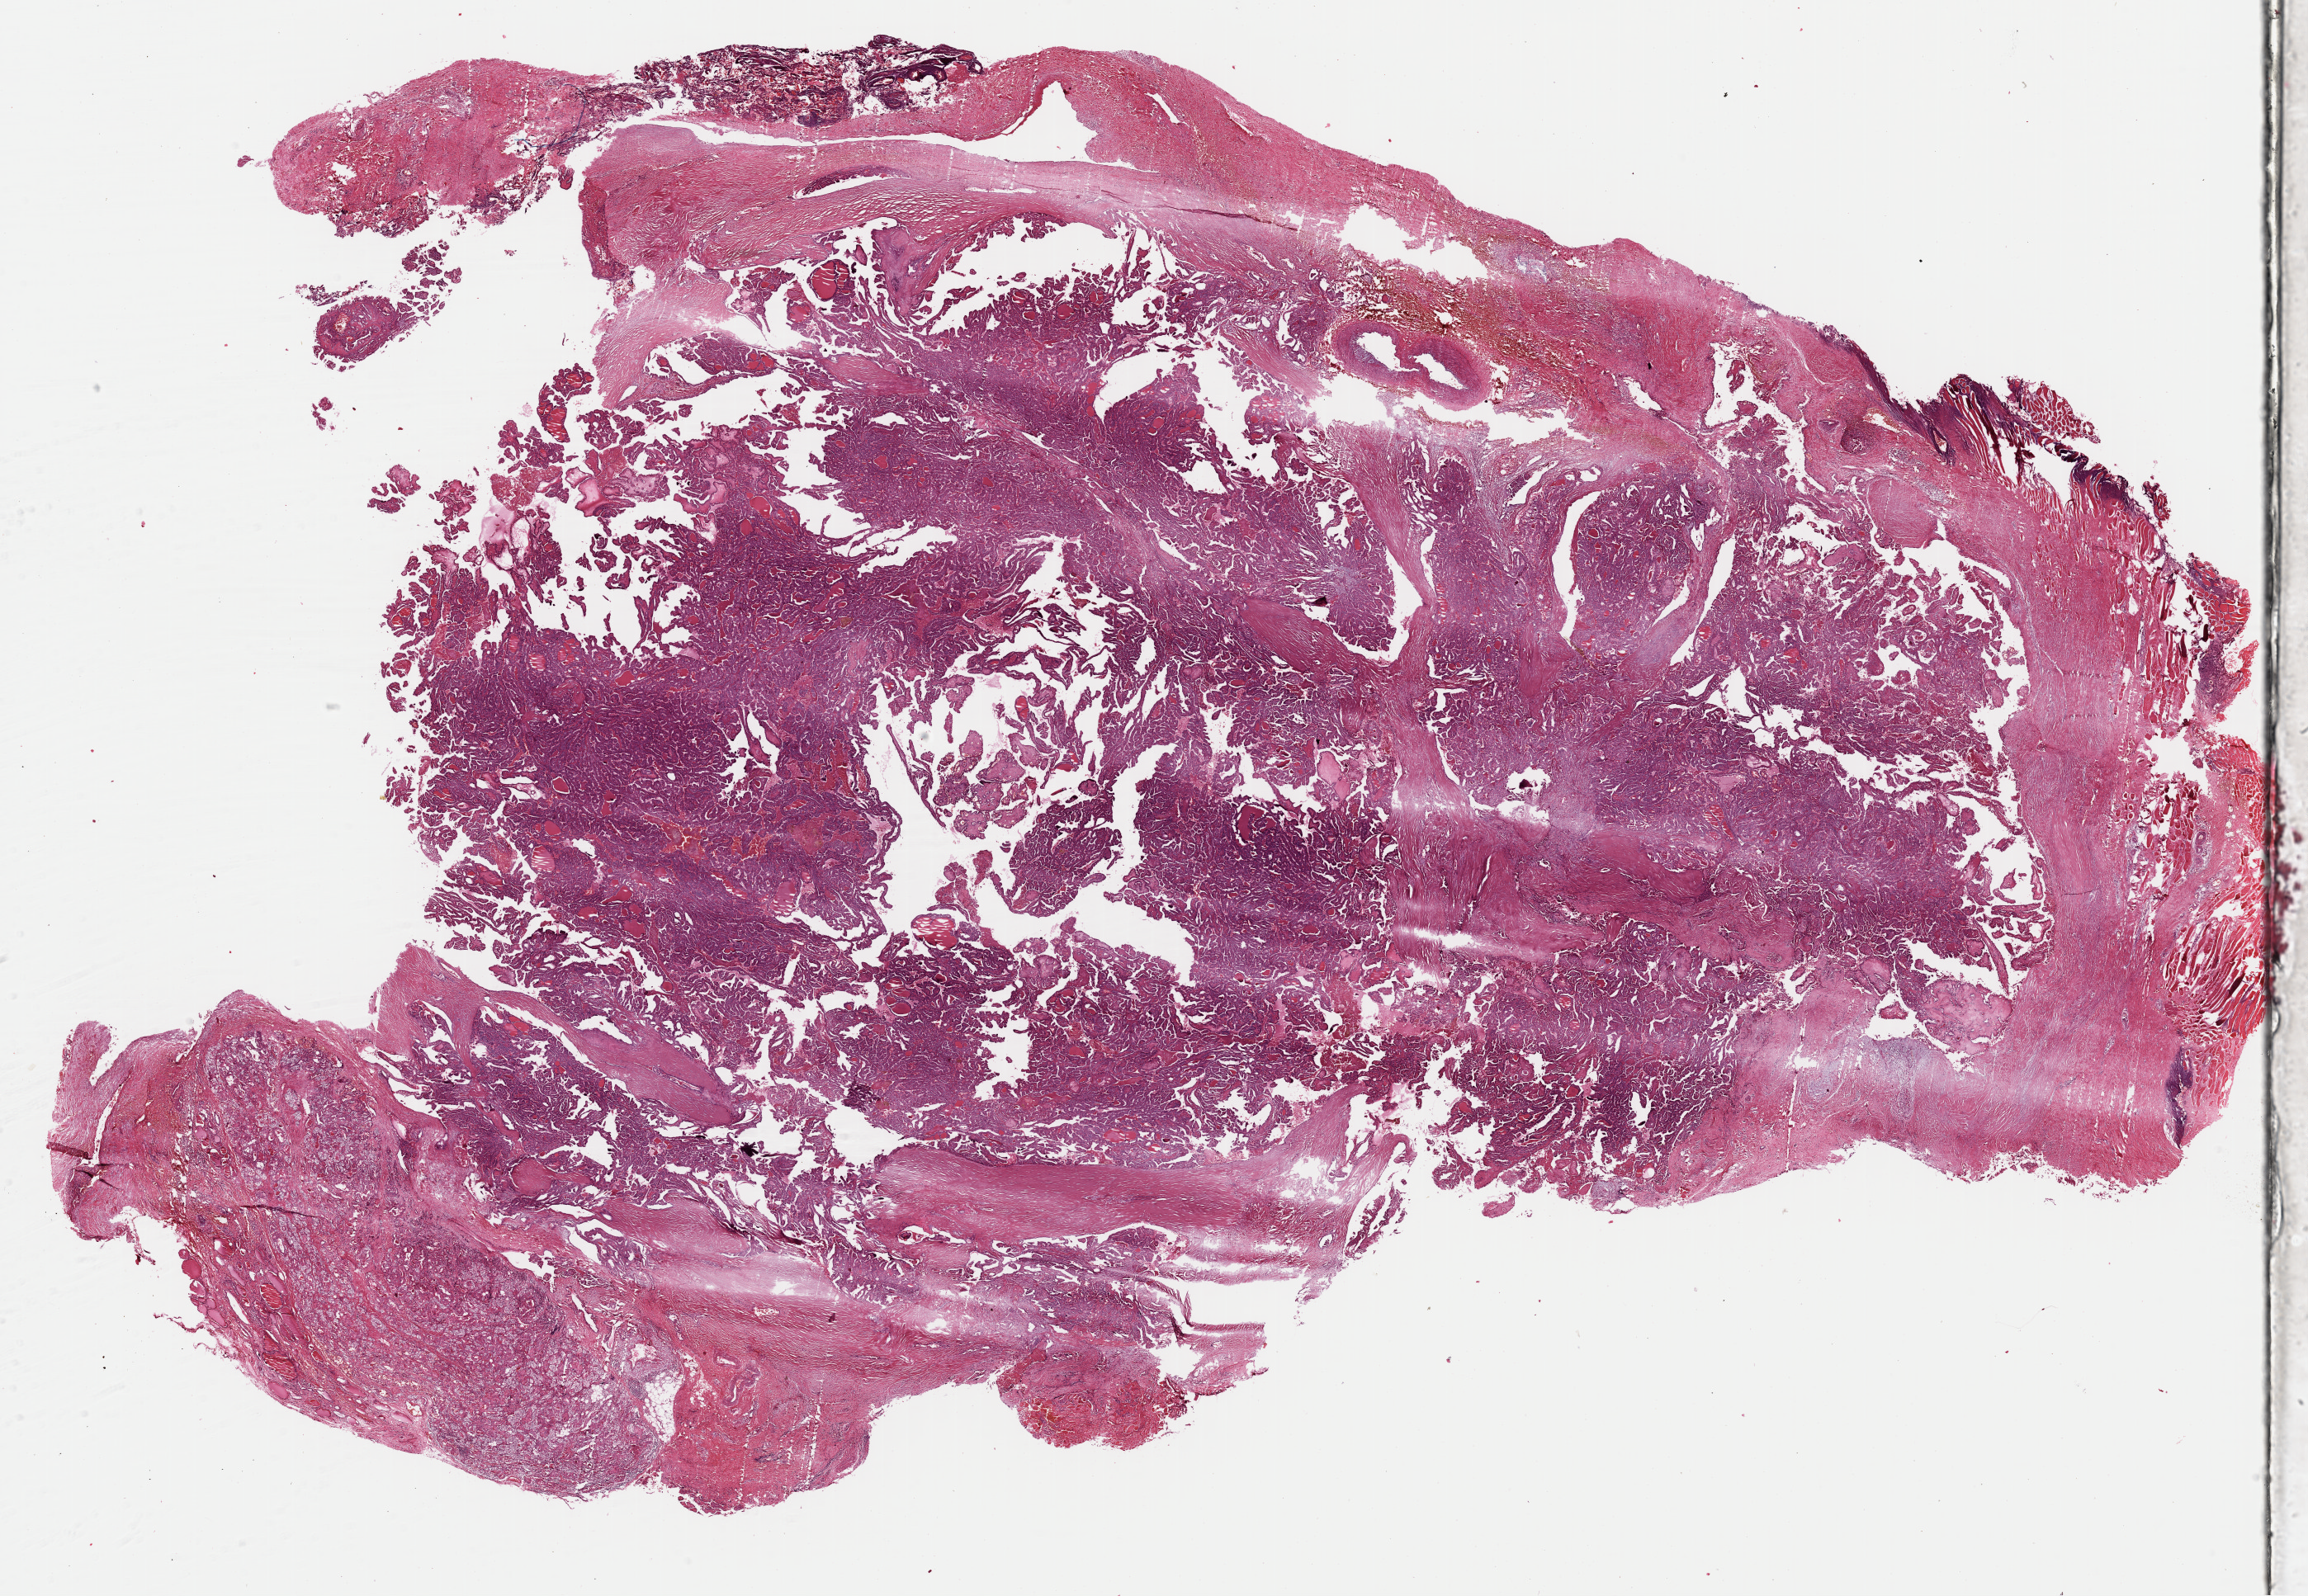
H&E-stained whole-slide image — whole scanned area (about 22.1 x 15.3 mm, acquisition: 40x scan) shown as a low-resolution overview. Formalin-fixed paraffin-embedded (FFPE) diagnostic section. Primary tumour sample from the thyroid. Female, age 34 years at initial diagnosis.
• laterality: left
• AJCC pathologic stage: I
• lymph nodes positive (case pathology): 4 of 7 examined
• histologic diagnosis: Papillary adenocarcinoma, NOS (thyroid gland)